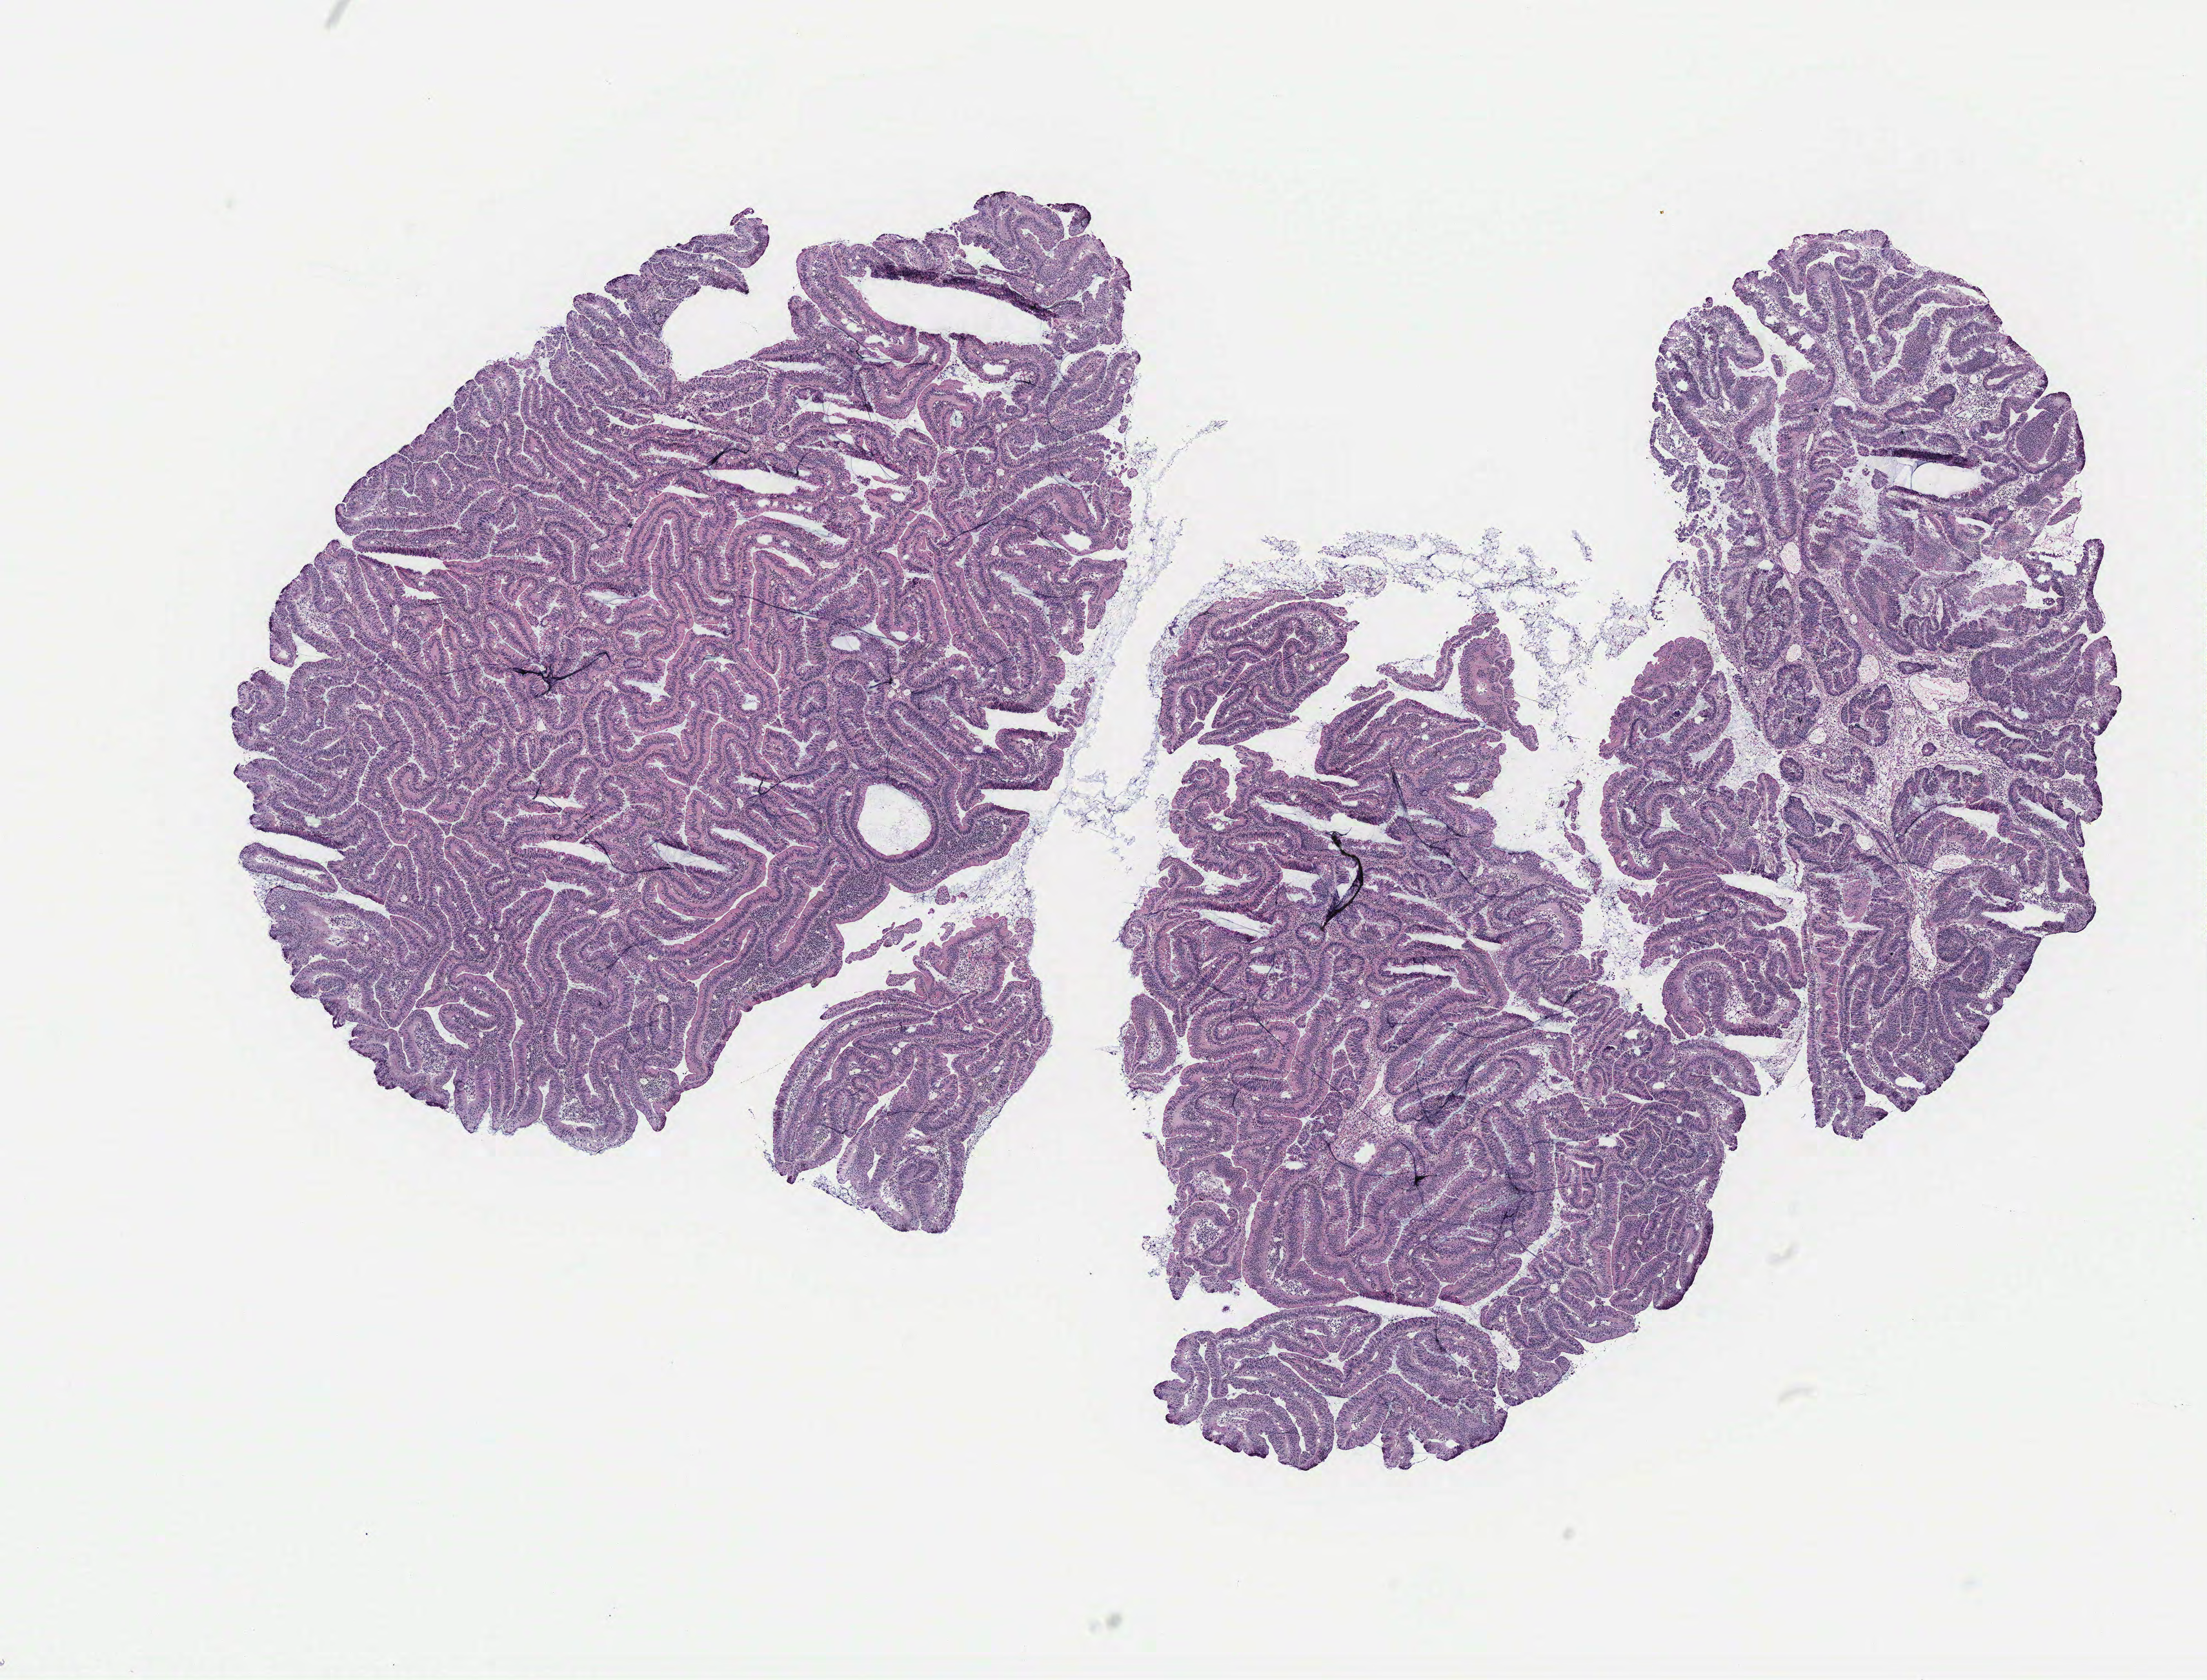
H&E-stained whole-slide image — a low-resolution overview of the entire scanned area, about 13.7 x 10.4 mm (from a 40x scan); colon, tissue type not recorded. Patient sex: female.
- patient diagnosis: Adenocarcinoma, NOS